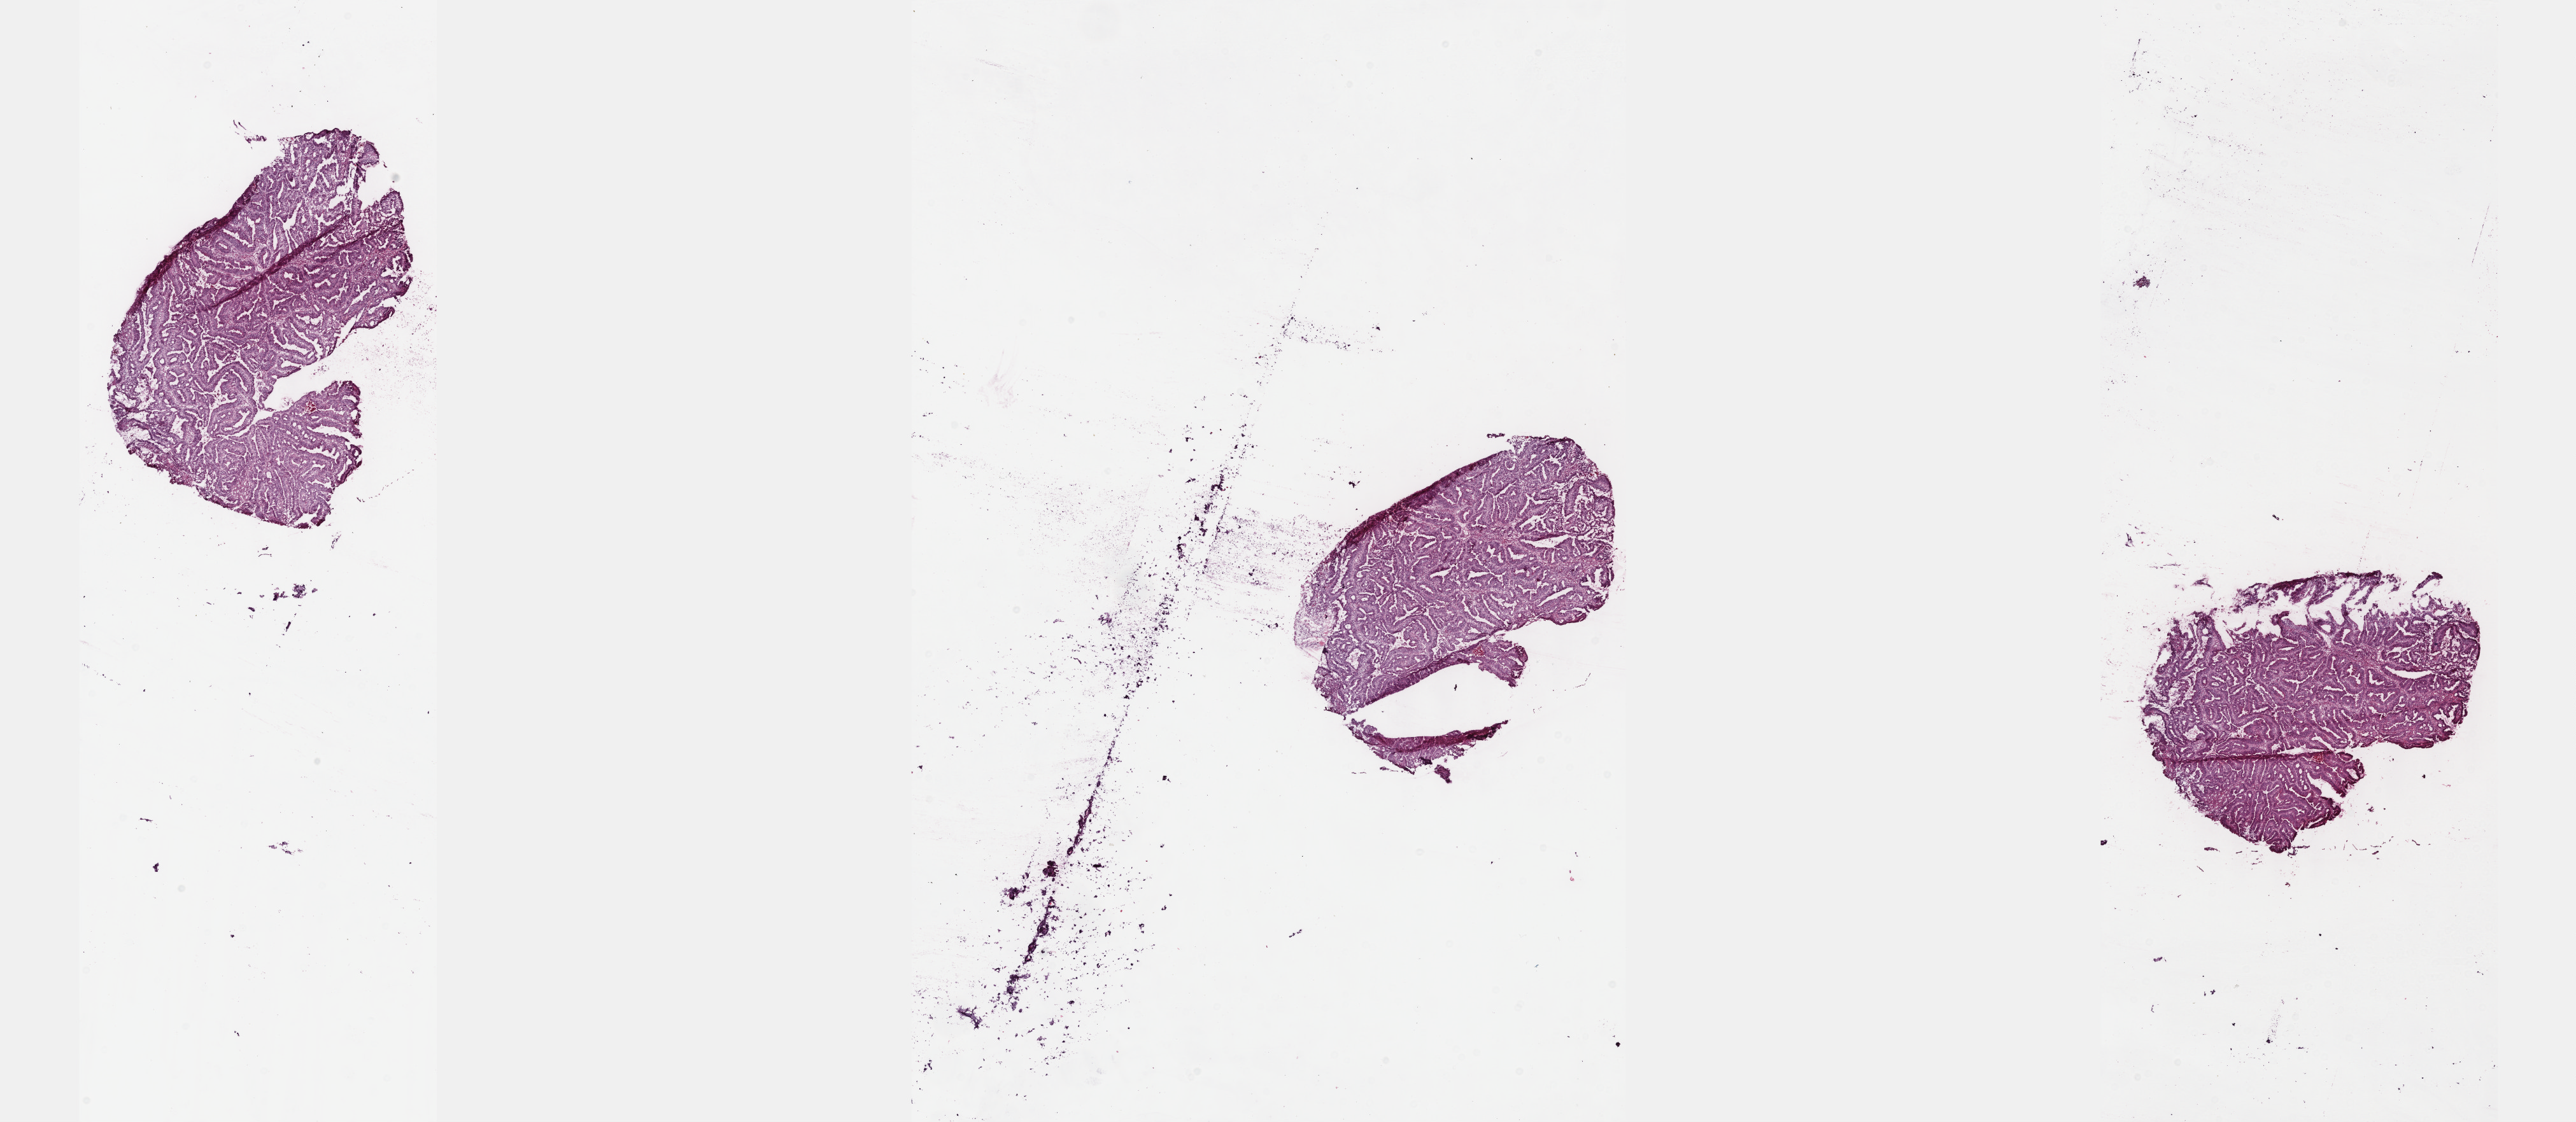
Whole-slide histology image, Hematoxylin and eosin (H&E) stained — shown as a low-resolution overview of the whole scanned area (about 32.7 x 14.2 mm, slide scanned at 40x); frozen section from the top of the tissue portion; colon, primary tumour sample. Patient: male, age at initial diagnosis 72 years. Slide review estimates, as recorded: tumour cells 97%, tumour nuclei 95%, normal cells 0%, stromal cells 2%, necrosis 1%. Inflammatory infiltration, as recorded: lymphocyte infiltration 2%, monocyte infiltration 1%, neutrophil infiltration 1%.
Diagnosis: Adenocarcinoma, NOS (sigmoid colon). AJCC pathologic stage: IIIB. Lymph nodes positive (case pathology): 2 of 30 examined.